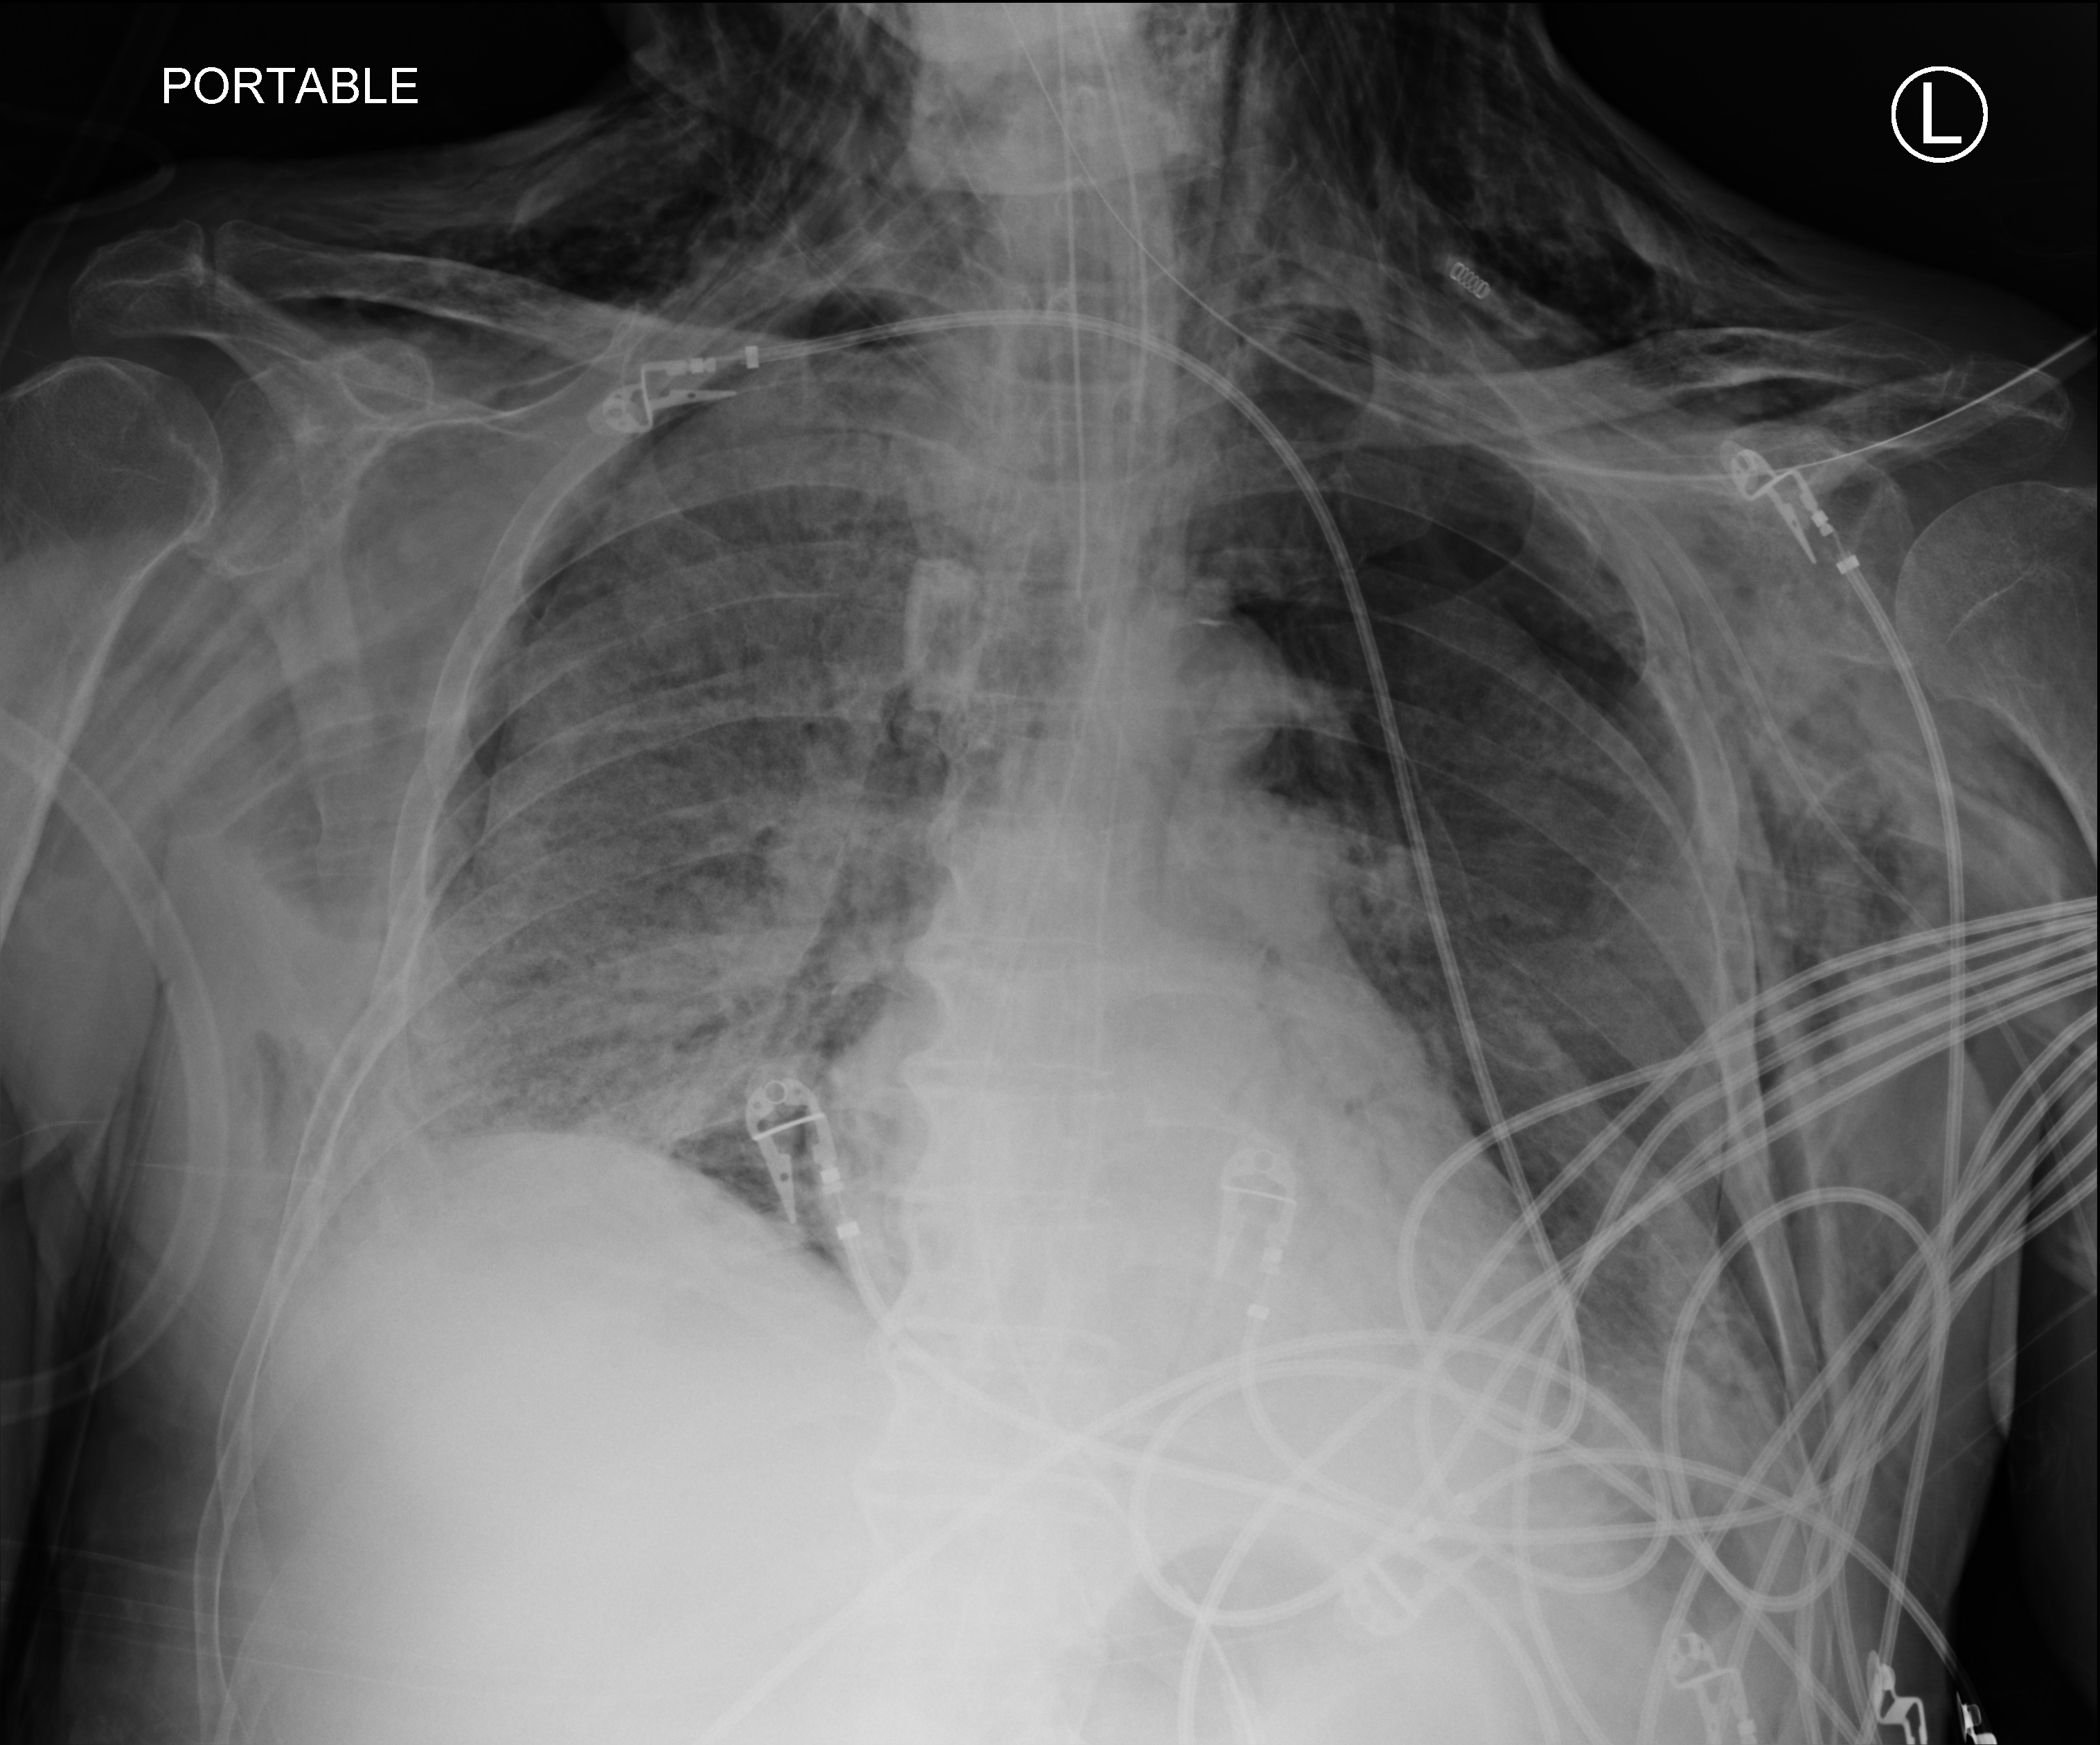
Bedside chest radiograph (computed radiography). Male patient hospitalised with COVID-19, age 75–90 years.
From the hospital-stay record, not from the radiograph (when in the stay this image was taken is not recorded):
- chronic kidney disease (admission record): no